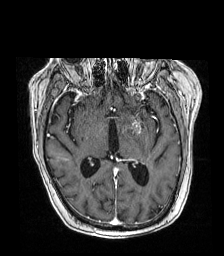
Brain MRI from a brain-tumour surgery series, one axial slice. Slice 93 of 192 in the series (ordered by position). T1-weighted post-contrast. 1 mm slice thickness. 224 × 256 image matrix, field of view 219 × 250 mm. Case-level facts recorded for this patient, not image findings: histopathology: Metastatic carcinoma from lung primary; tumour location: Left Frontal Caudate.
Annotated regions visible in this slice (manually delineated by an expert):
- tumour: box from (x=135, y=118) to (x=145, y=130) px